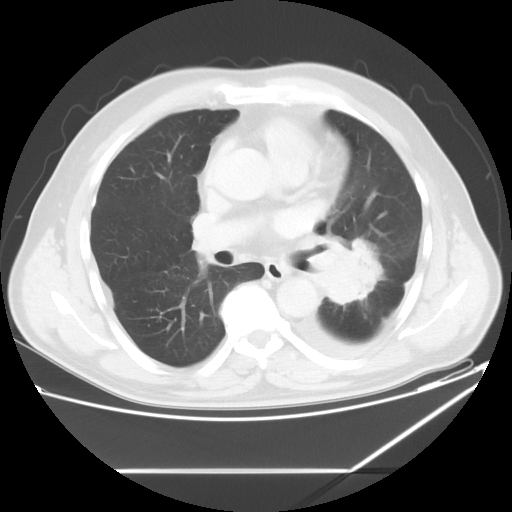
Chest CT, one axial slice; slice 32 of 60 in the series (ordered by position); reconstruction kernel STANDARD; lung window (W 1500 / L -600 HU); 5 mm slice thickness; 512 × 512 image matrix. Male patient, age 62 years. Case-level facts recorded for this patient, not image findings: clinical TNM (as recorded): T3 N0 M1.
Structures marked on this image (rectangle marked by the reading radiologist):
- lung tumour (recorded histology: adenocarcinoma): bounding box <310,231,387,304> (left, top, right, bottom; pixels)
- lung tumour (recorded histology: adenocarcinoma): <321,235,382,311>